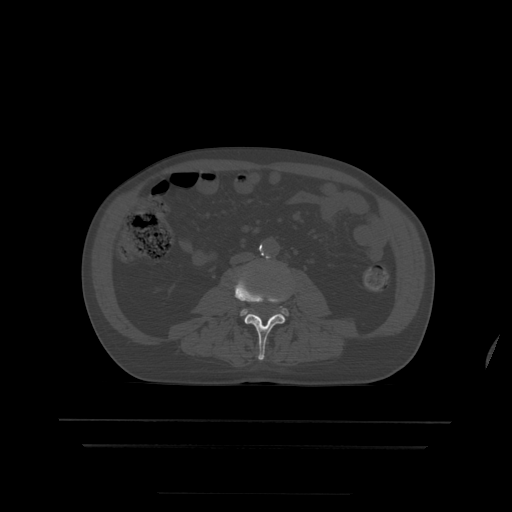
CT including the spine, one axial slice; position 112 of 522 along the scan axis; bone window (W 1800 / L 400 HU); 512 × 512 image matrix, field of view 436 × 436 mm. Patient age 68 years. From the clinical record (not read from this slice): primary cancer: urothelial.
Structures marked on this image (semi-automatically segmented with operator editing):
- L3 vertebra: box from (x=235, y=273) to (x=288, y=361) px
- L4 vertebra: (x=241, y=309)–(x=289, y=316)